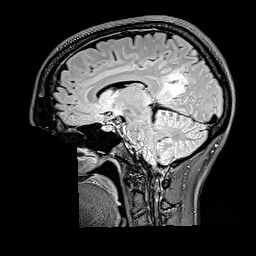
Brain MRI from a brain-tumour surgery series, one sagittal slice; T2 FLAIR; 1 mm slice thickness; 256 × 256 image matrix, field of view 256 × 256 mm. Case-level facts recorded for this patient, not image findings: histopathology: Oligodendroglioma; WHO grade: 2.
Structures marked on this image (expert manual segmentation):
- tumour: bounding box [x1, y1, x2, y2] px = [159, 68, 189, 104]